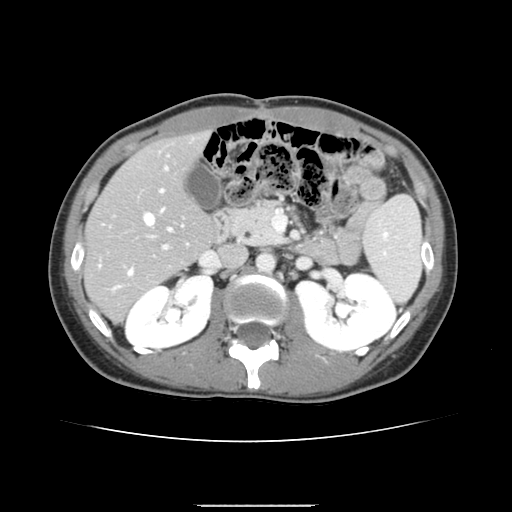
Contrast-enhanced abdominal CT, one axial slice. Slice 77 of 150 in the series (ordered by position). 120 kVp. Soft-tissue window (W 400 / L 40 HU). 512 × 512 image matrix, field of view 324 × 324 mm. Female patient, age 32 years. Case-level facts recorded for this patient, not image findings: diagnosis: colorectal cancer liver metastases, imaged before liver resection; multiple liver metastases: yes; largest metastasis: 0.7 cm; chemotherapy before resection: yes.
Outlined on this slice (manually delineated by an expert):
- hepatic veins: box from (x=128, y=209) to (x=172, y=275) px
- liver: (x=85, y=133)–(x=214, y=319)
- planned liver remnant (the part of the liver to remain after resection): (x=87, y=133)–(x=214, y=279)
- portal vein (with intrahepatic branches): (x=114, y=166)–(x=183, y=289)